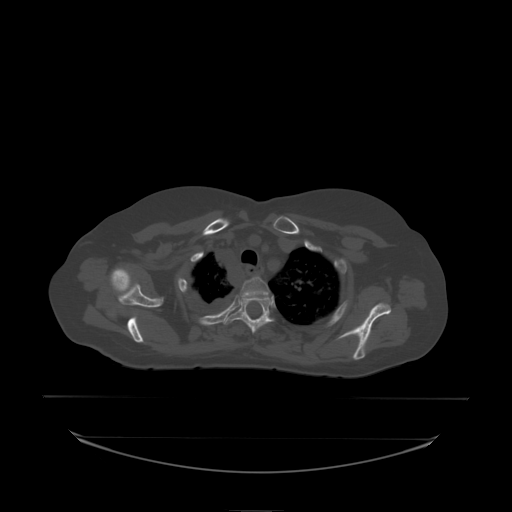
CT including the spine, one axial slice. Position 175 of 242 along the scan axis. Bone window (W 1800 / L 400 HU). 2.5 mm slice thickness. 512 × 512 image matrix, field of view 500 × 500 mm. Patient: female, 53 years. From the clinical record (not read from this slice): primary cancer: lung; vertebrae with lytic lesions (as recorded): T7, L1.
Annotated regions visible in this slice (semi-automatically segmented with operator editing):
- T2 vertebra: bounding box <240,277,270,302> (left, top, right, bottom; pixels)
- T3 vertebra: <224,298,274,333>